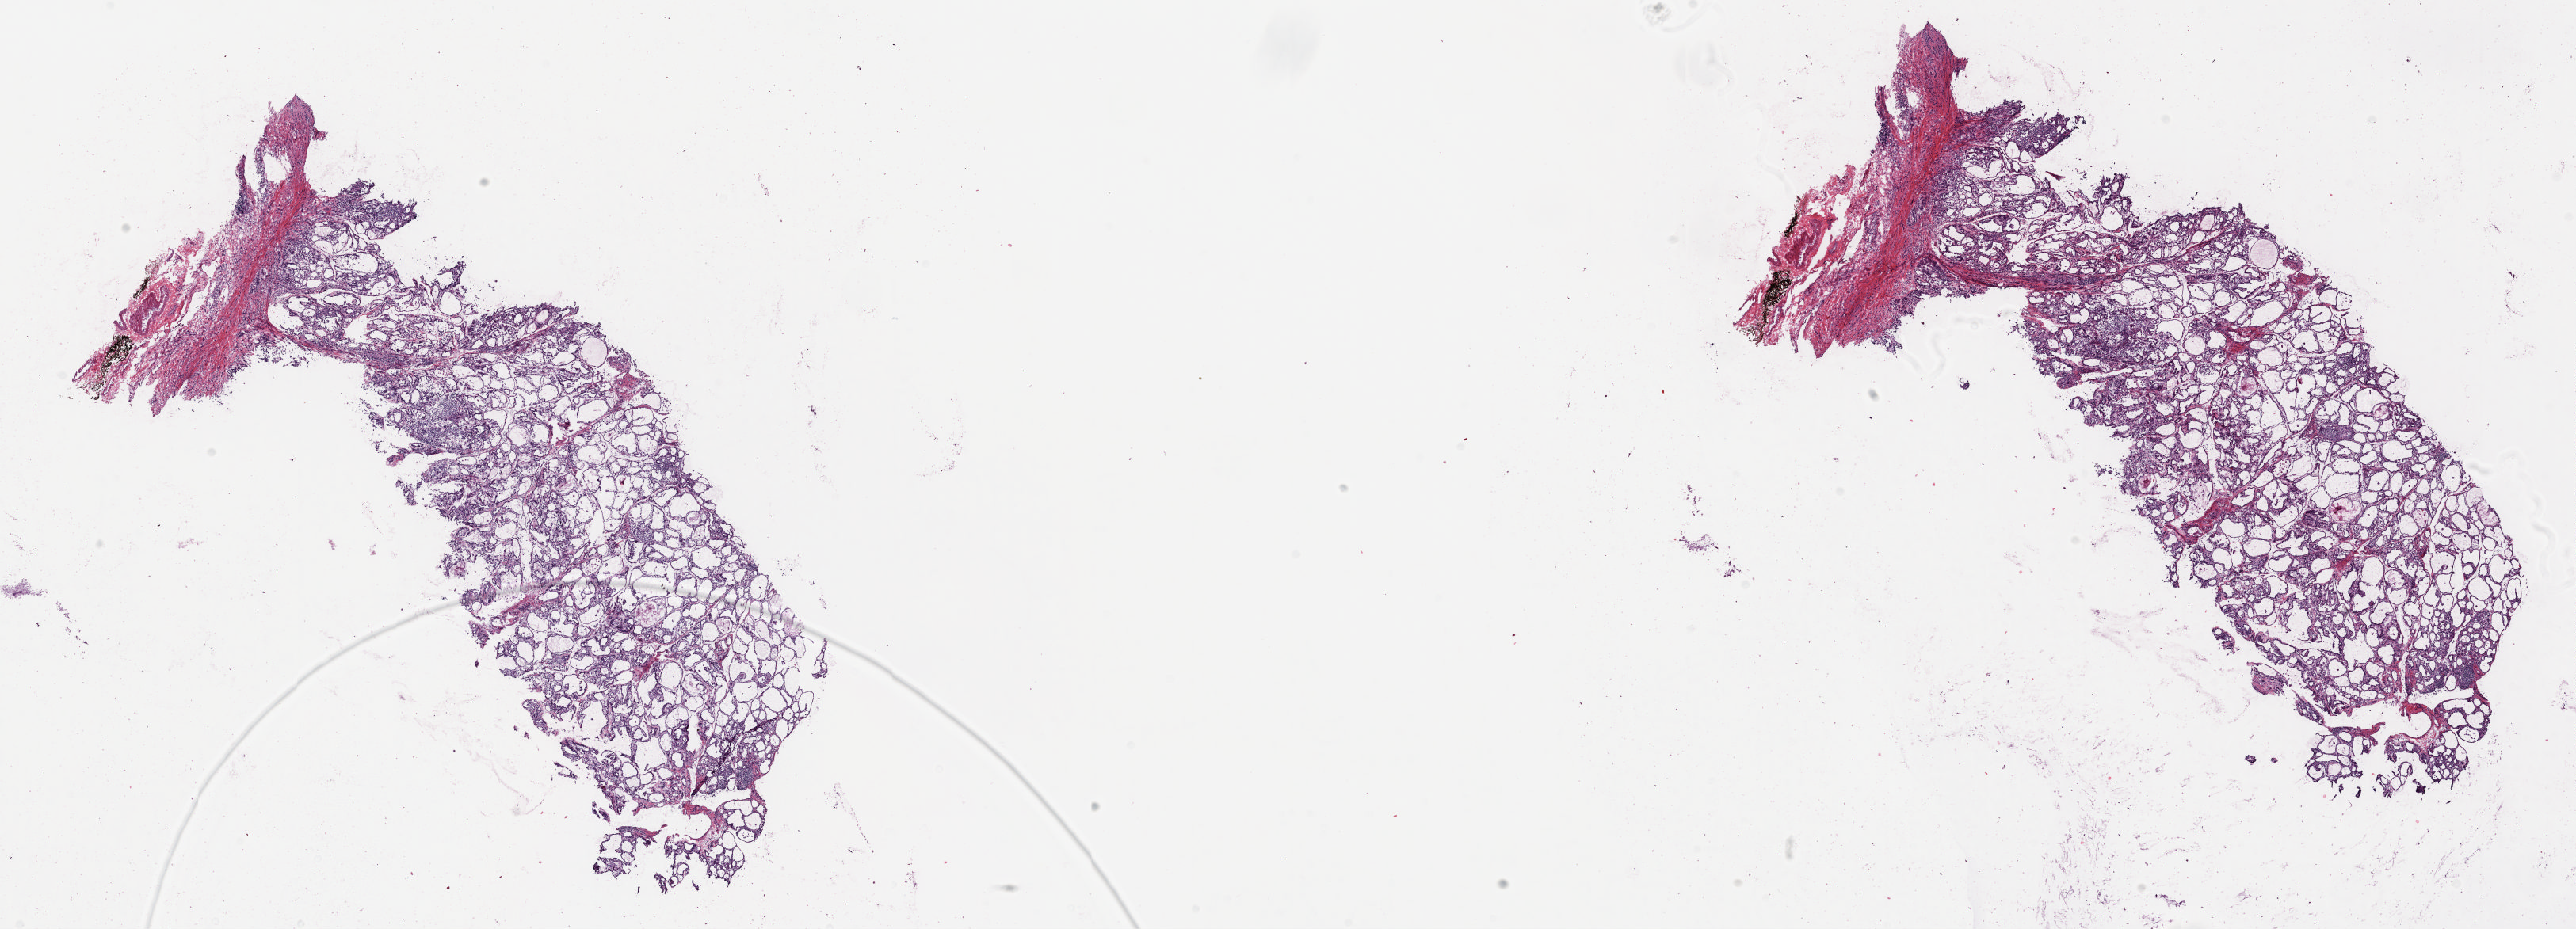
Digitized H&E tissue section (whole slide) — shown as a low-resolution overview of the whole scanned area (about 25.8 x 9.3 mm, slide scanned at 20x), frozen section, solid tissue normal (non-tumour tissue) sample from the thyroid. Patient: female, age at initial diagnosis 34 years. Pathologist review of this section (percent, as recorded): tumour cells 0%, tumour nuclei 0%, normal cells 60%, stromal cells 40%, necrosis 0%. Inflammatory infiltration, as recorded: lymphocyte infiltration 15%, monocyte infiltration 0%, neutrophil infiltration 0%.
This section: solid tissue normal sample (biorepository sample class). Patient diagnosis: Papillary adenocarcinoma, NOS (thyroid gland).